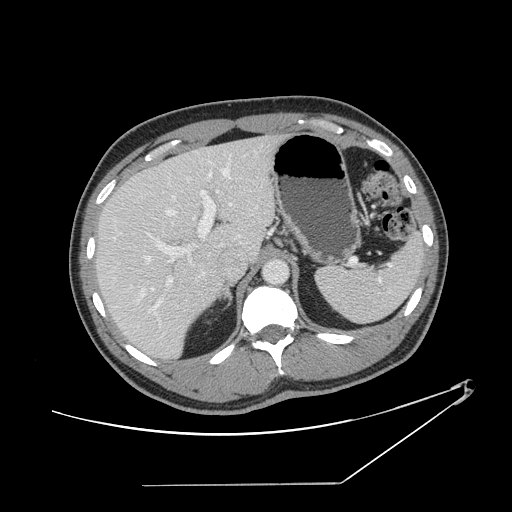
Contrast-enhanced abdominal CT, one axial slice; slice 97 of 152 in the series (ordered by position); 120 kVp; soft-tissue window (W 400 / L 40 HU); 2.5 mm slice thickness; 512 × 512 image matrix. Male patient, age 45 years. From the clinical record (not read from this slice): diagnosis: colorectal cancer liver metastases, imaged before liver resection; multiple liver metastases: no; largest metastasis: 1 cm.
Annotated regions visible in this slice (outlined manually by an expert reader):
- hepatic veins: box from (x=111, y=154) to (x=233, y=297) px
- liver: (x=98, y=137)–(x=277, y=358)
- planned liver remnant (the part of the liver to remain after resection): (x=97, y=154)–(x=229, y=358)
- portal vein (with intrahepatic branches): (x=146, y=172)–(x=215, y=326)